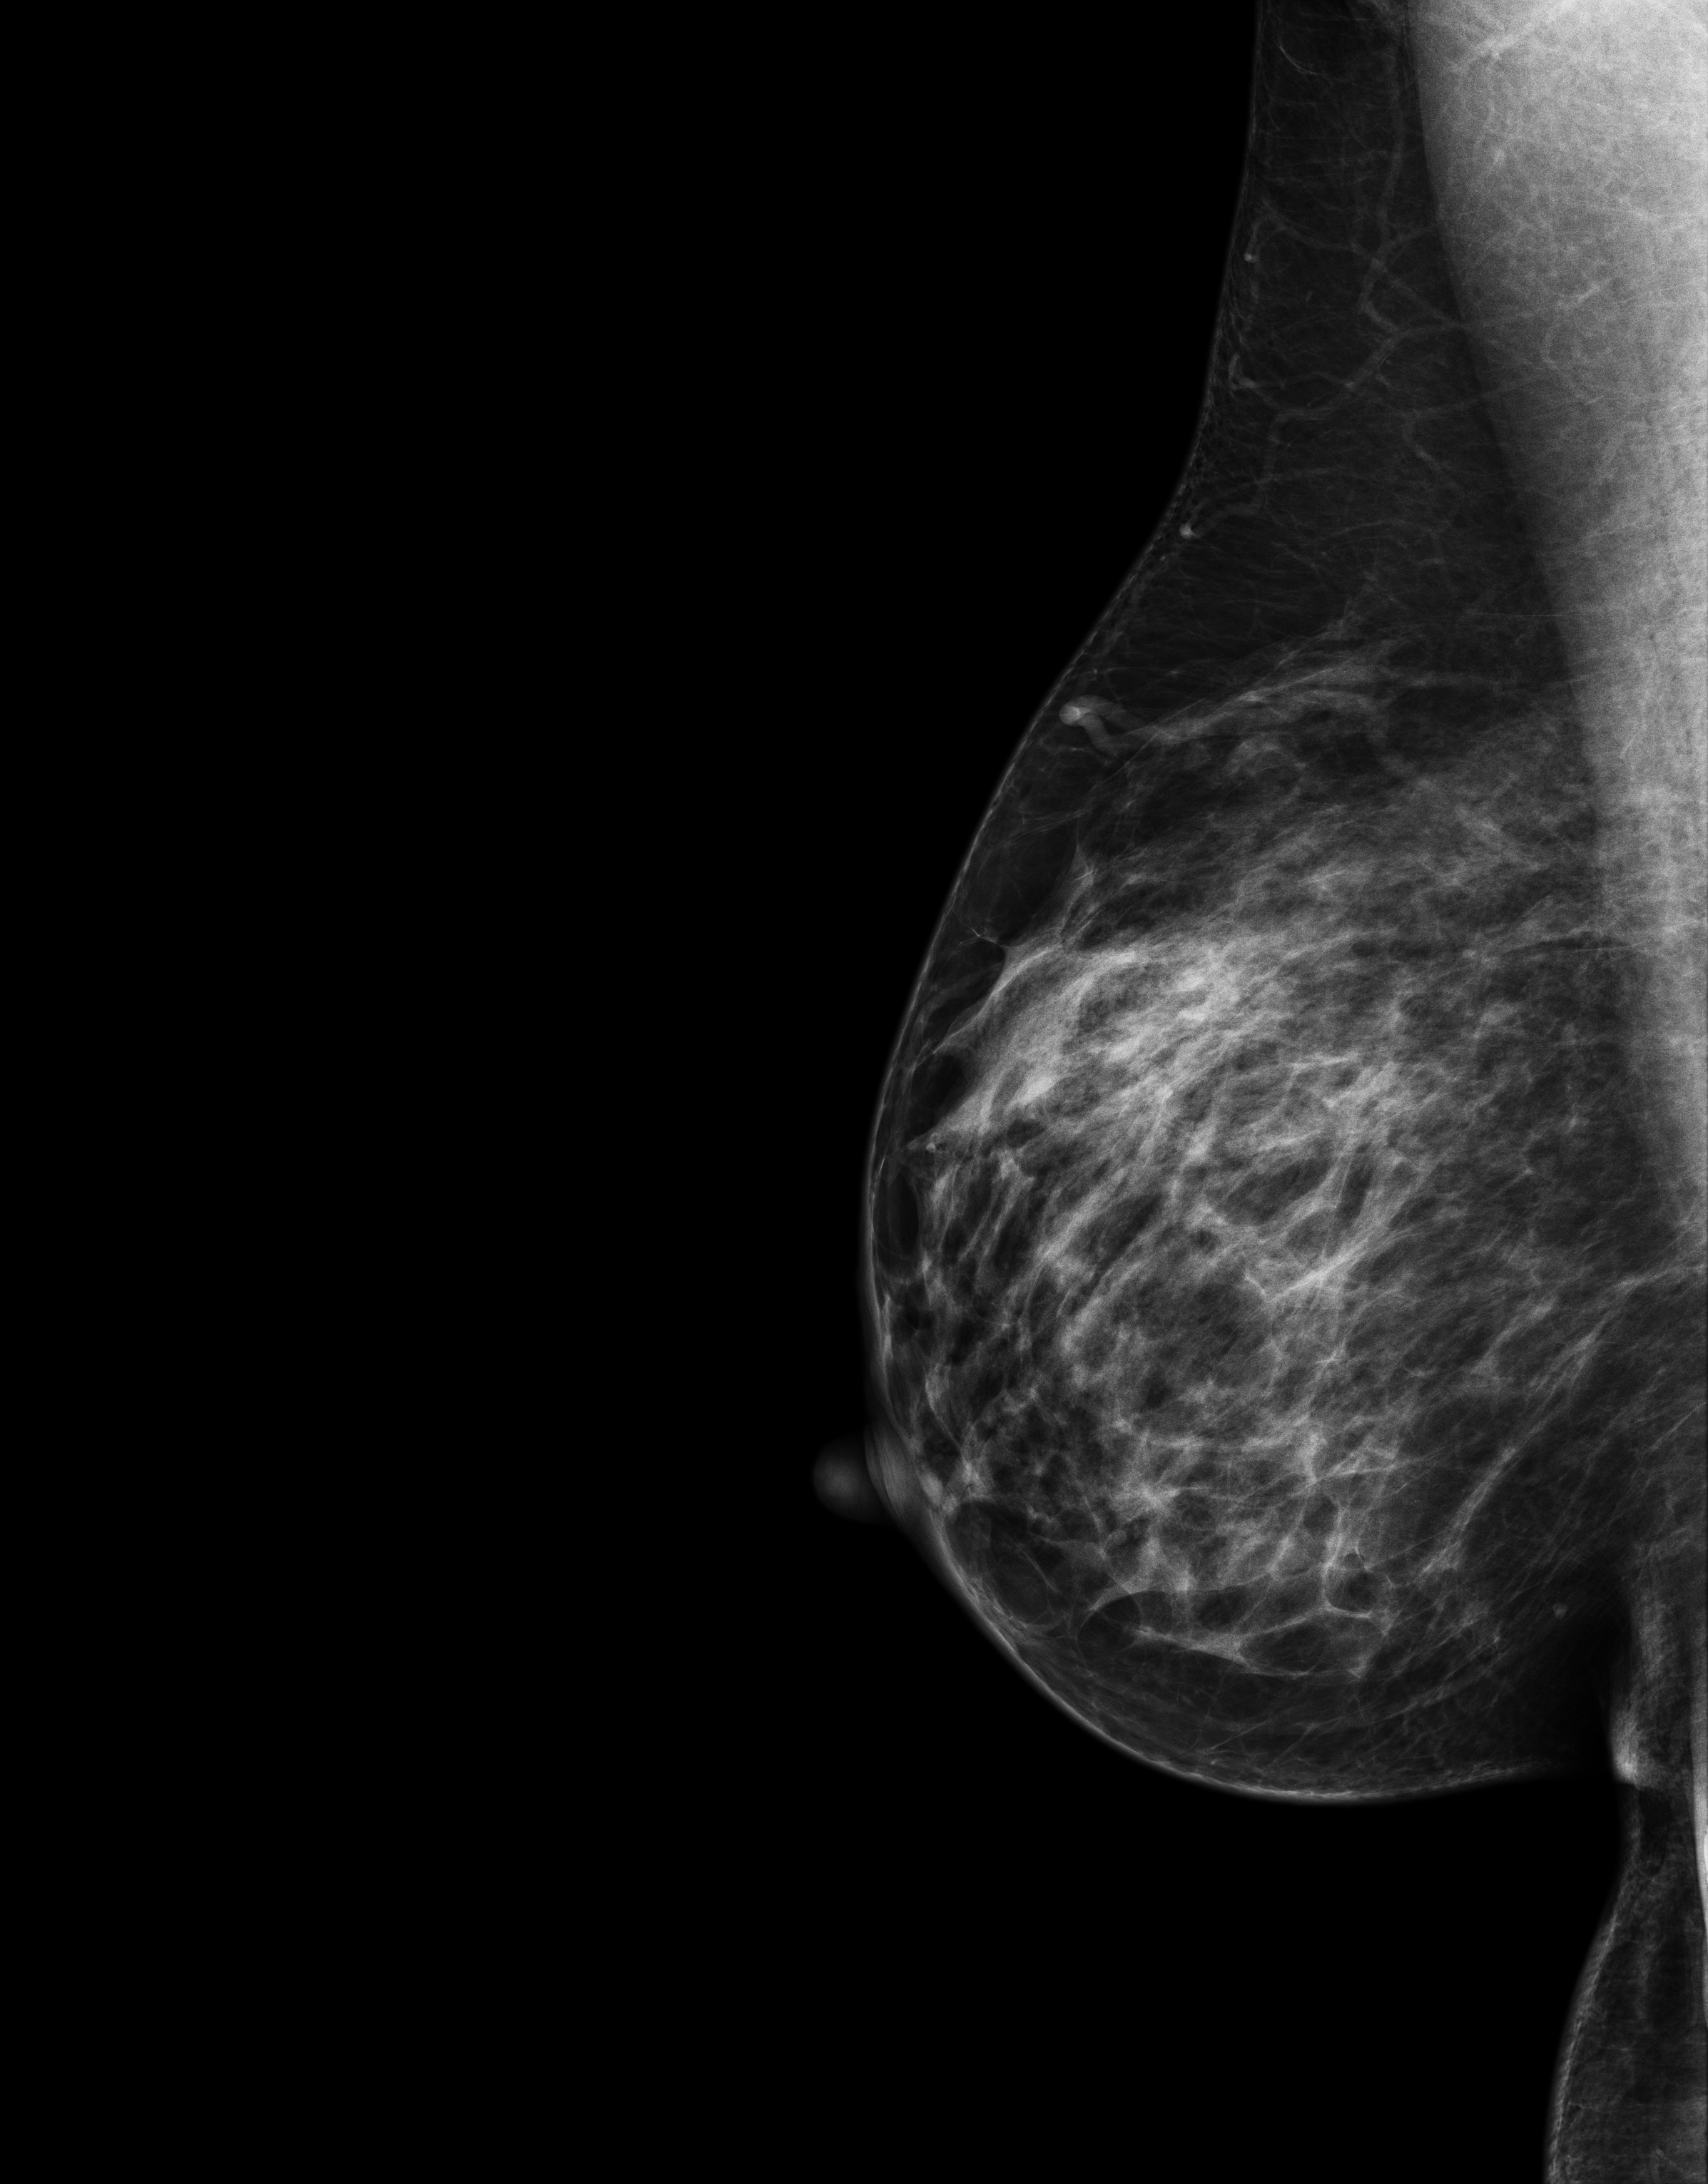
Digital mammogram (FFDM); right breast; medio-lateral oblique projection; annual screening mammography examination; compressed breast thickness 70 mm. Patient aged 49 years (female).
Breast density at the screening exam (both breasts): heterogeneously dense (BI-RADS density category c). Final BI-RADS assessment for this screening round (tomosynthesis exam, both breasts): category 1. Recall: no recall after this screen.